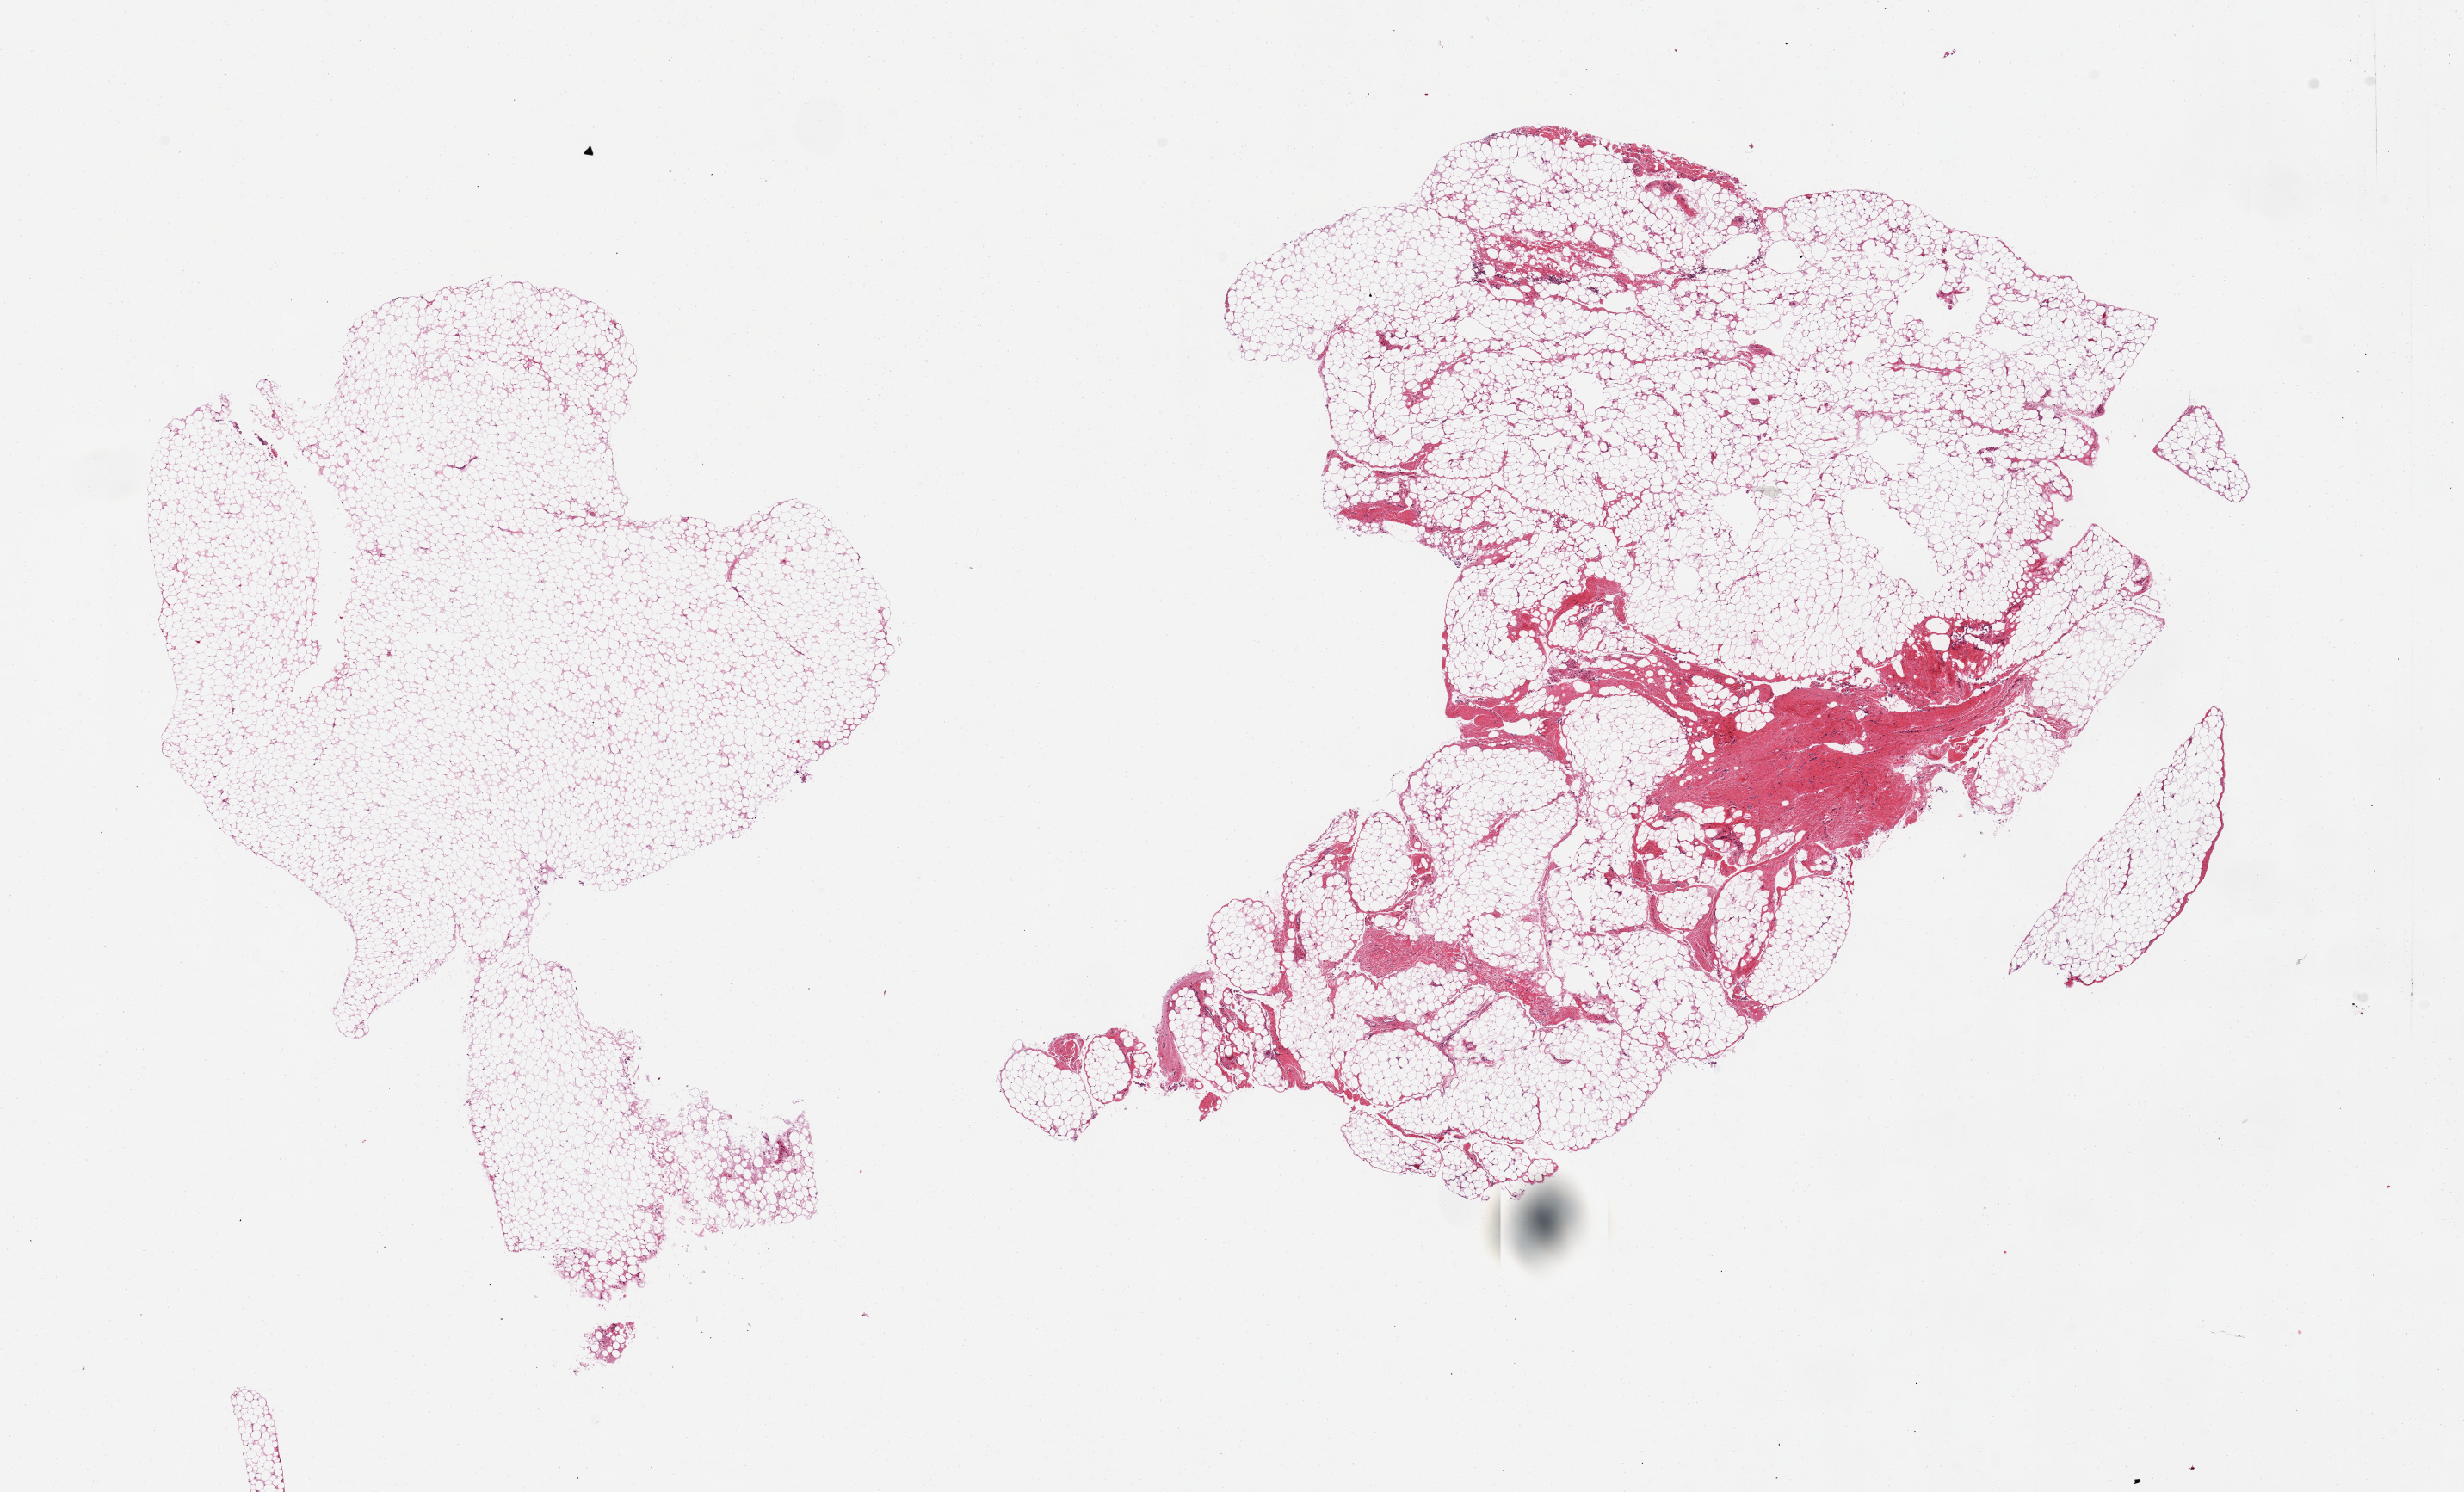
Digitized haematoxylin and eosin-stained section — low-resolution overview of the scanned area, about 22.6 x 13.7 mm (from a 20x scan). PAXgene-fixed paraffin-embedded (PFPE) section. Target tissue: omentum. Donor tissue sample. Donor: male.
• review note (as recorded): 2 pieces: one with 10% fibrous content